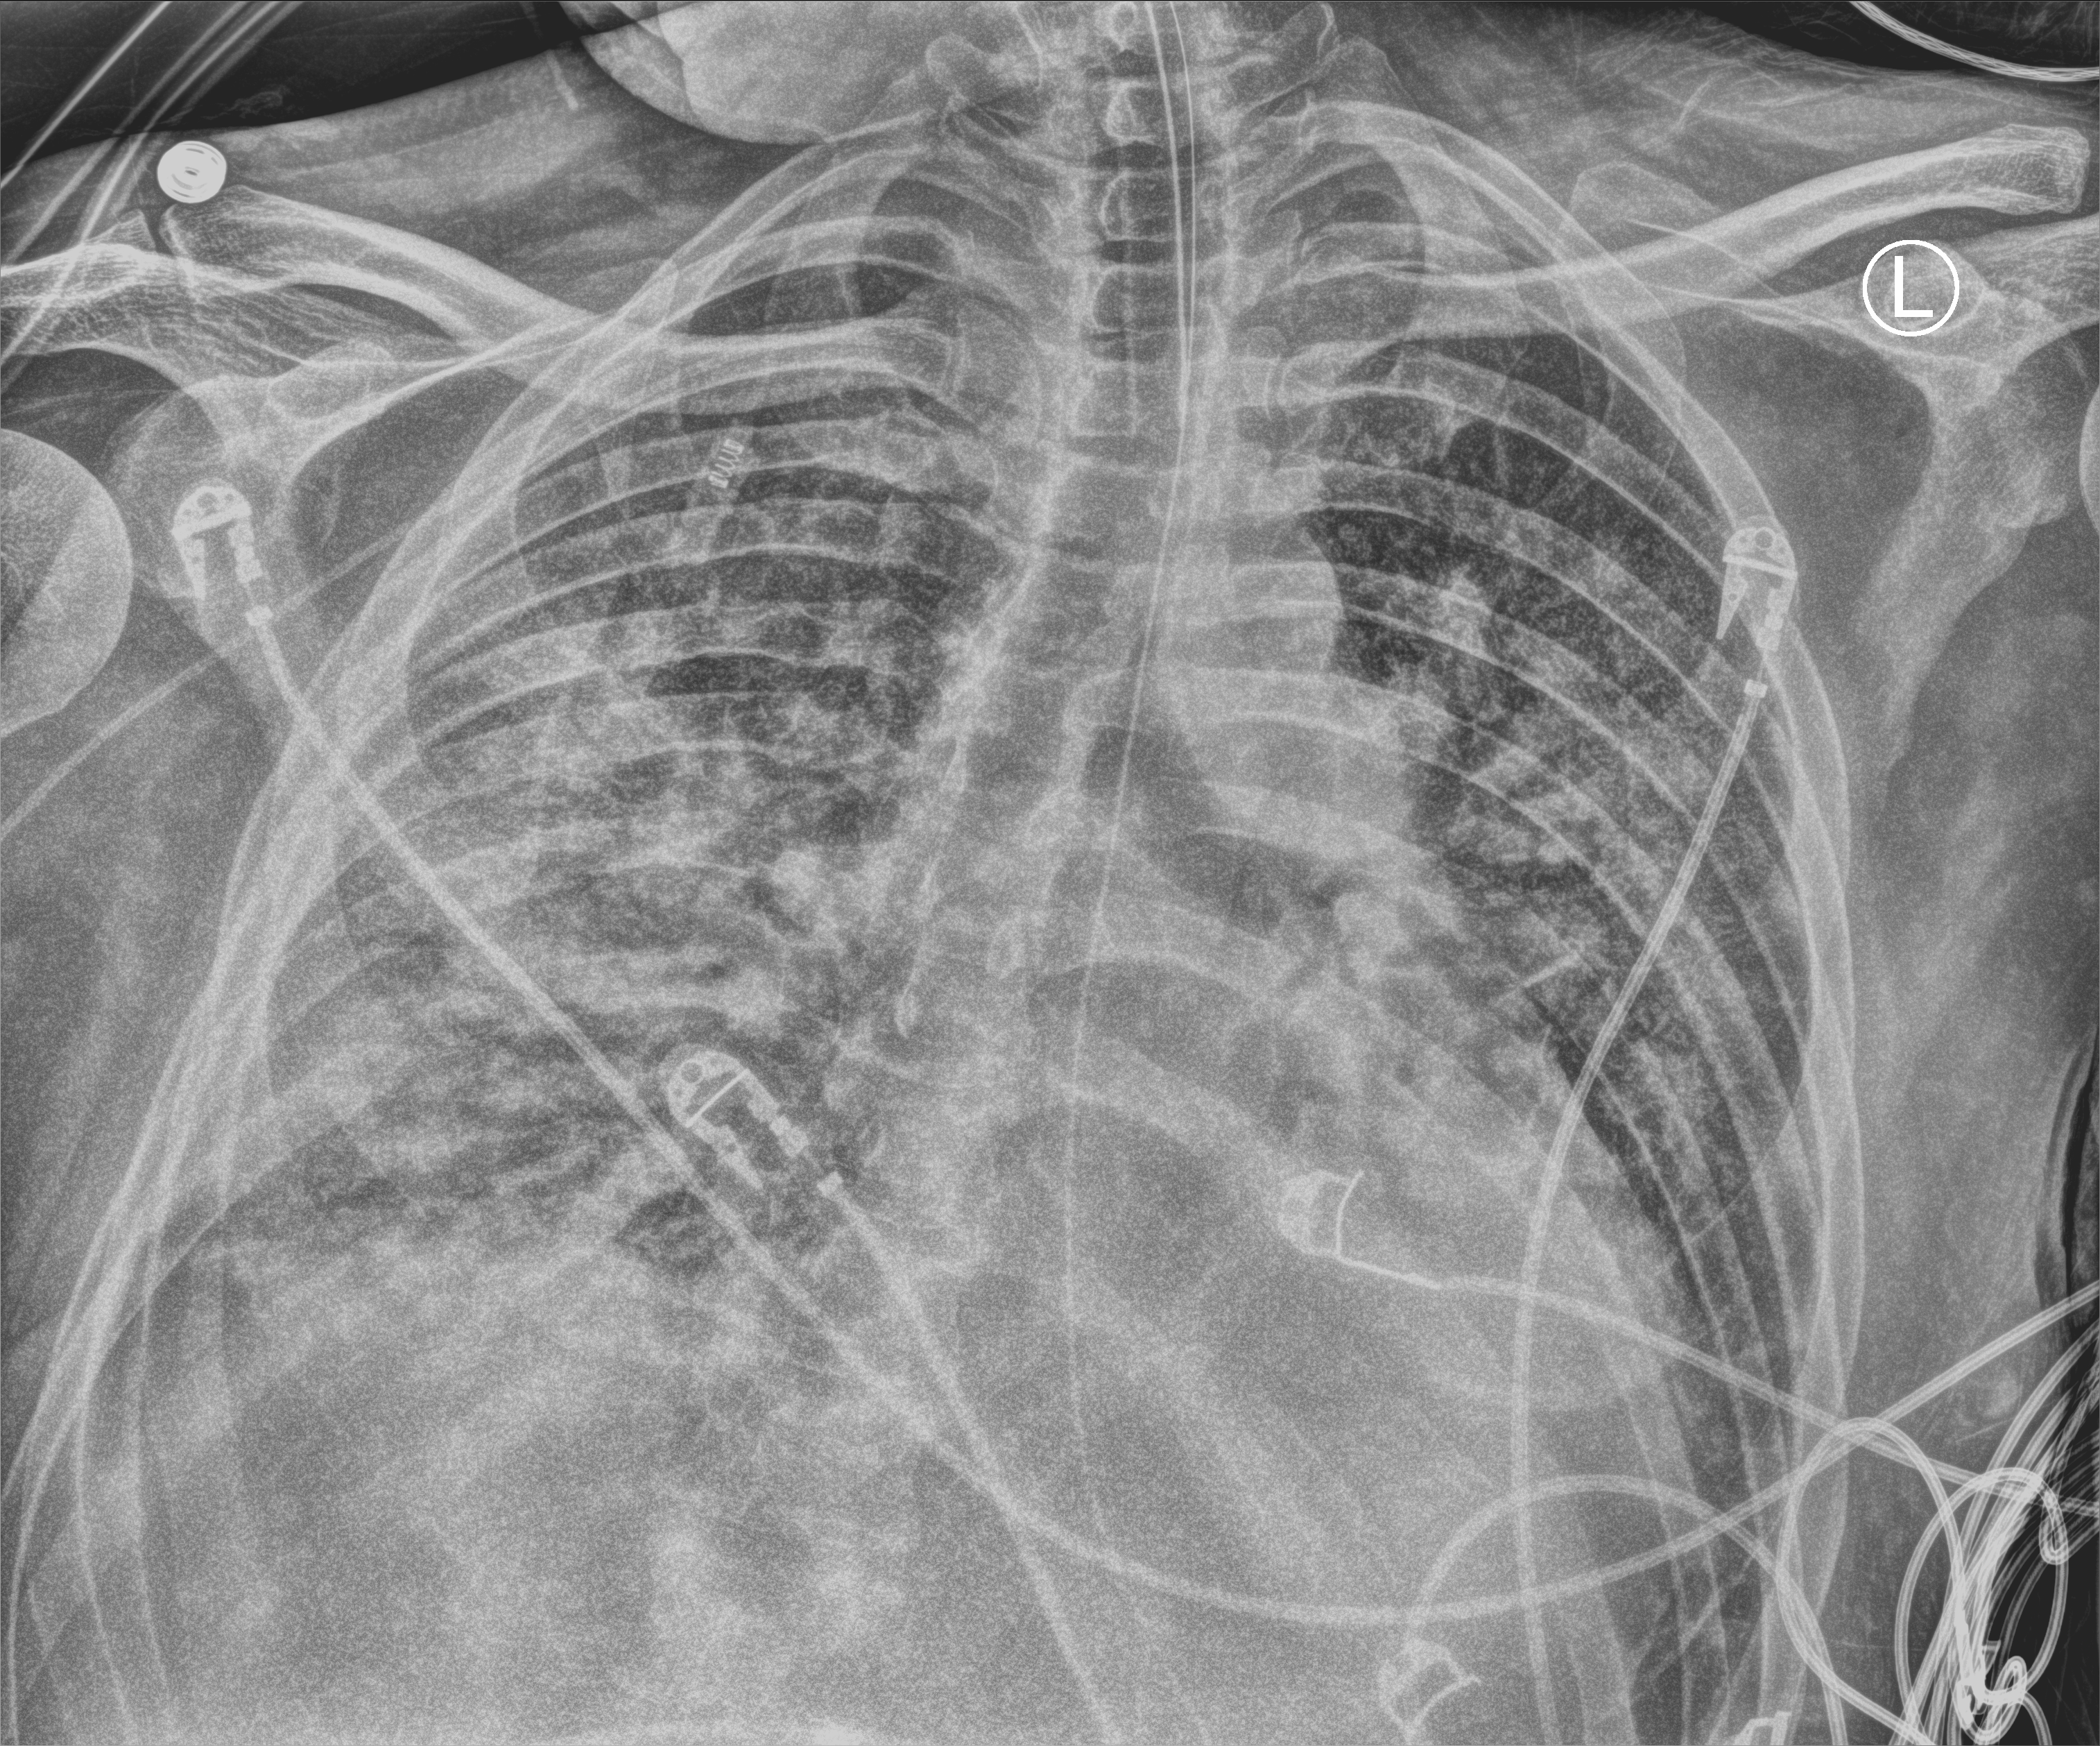
Chest X-ray (portable). Patient hospitalised with COVID-19; male, aged 18–59 years.
Admission-level facts for this patient (not findings on this image; timing relative to this image not recorded):
- mechanically ventilated during this hospital stay: yes
- smoking status (admission record): never
- length of hospital stay: 75 days